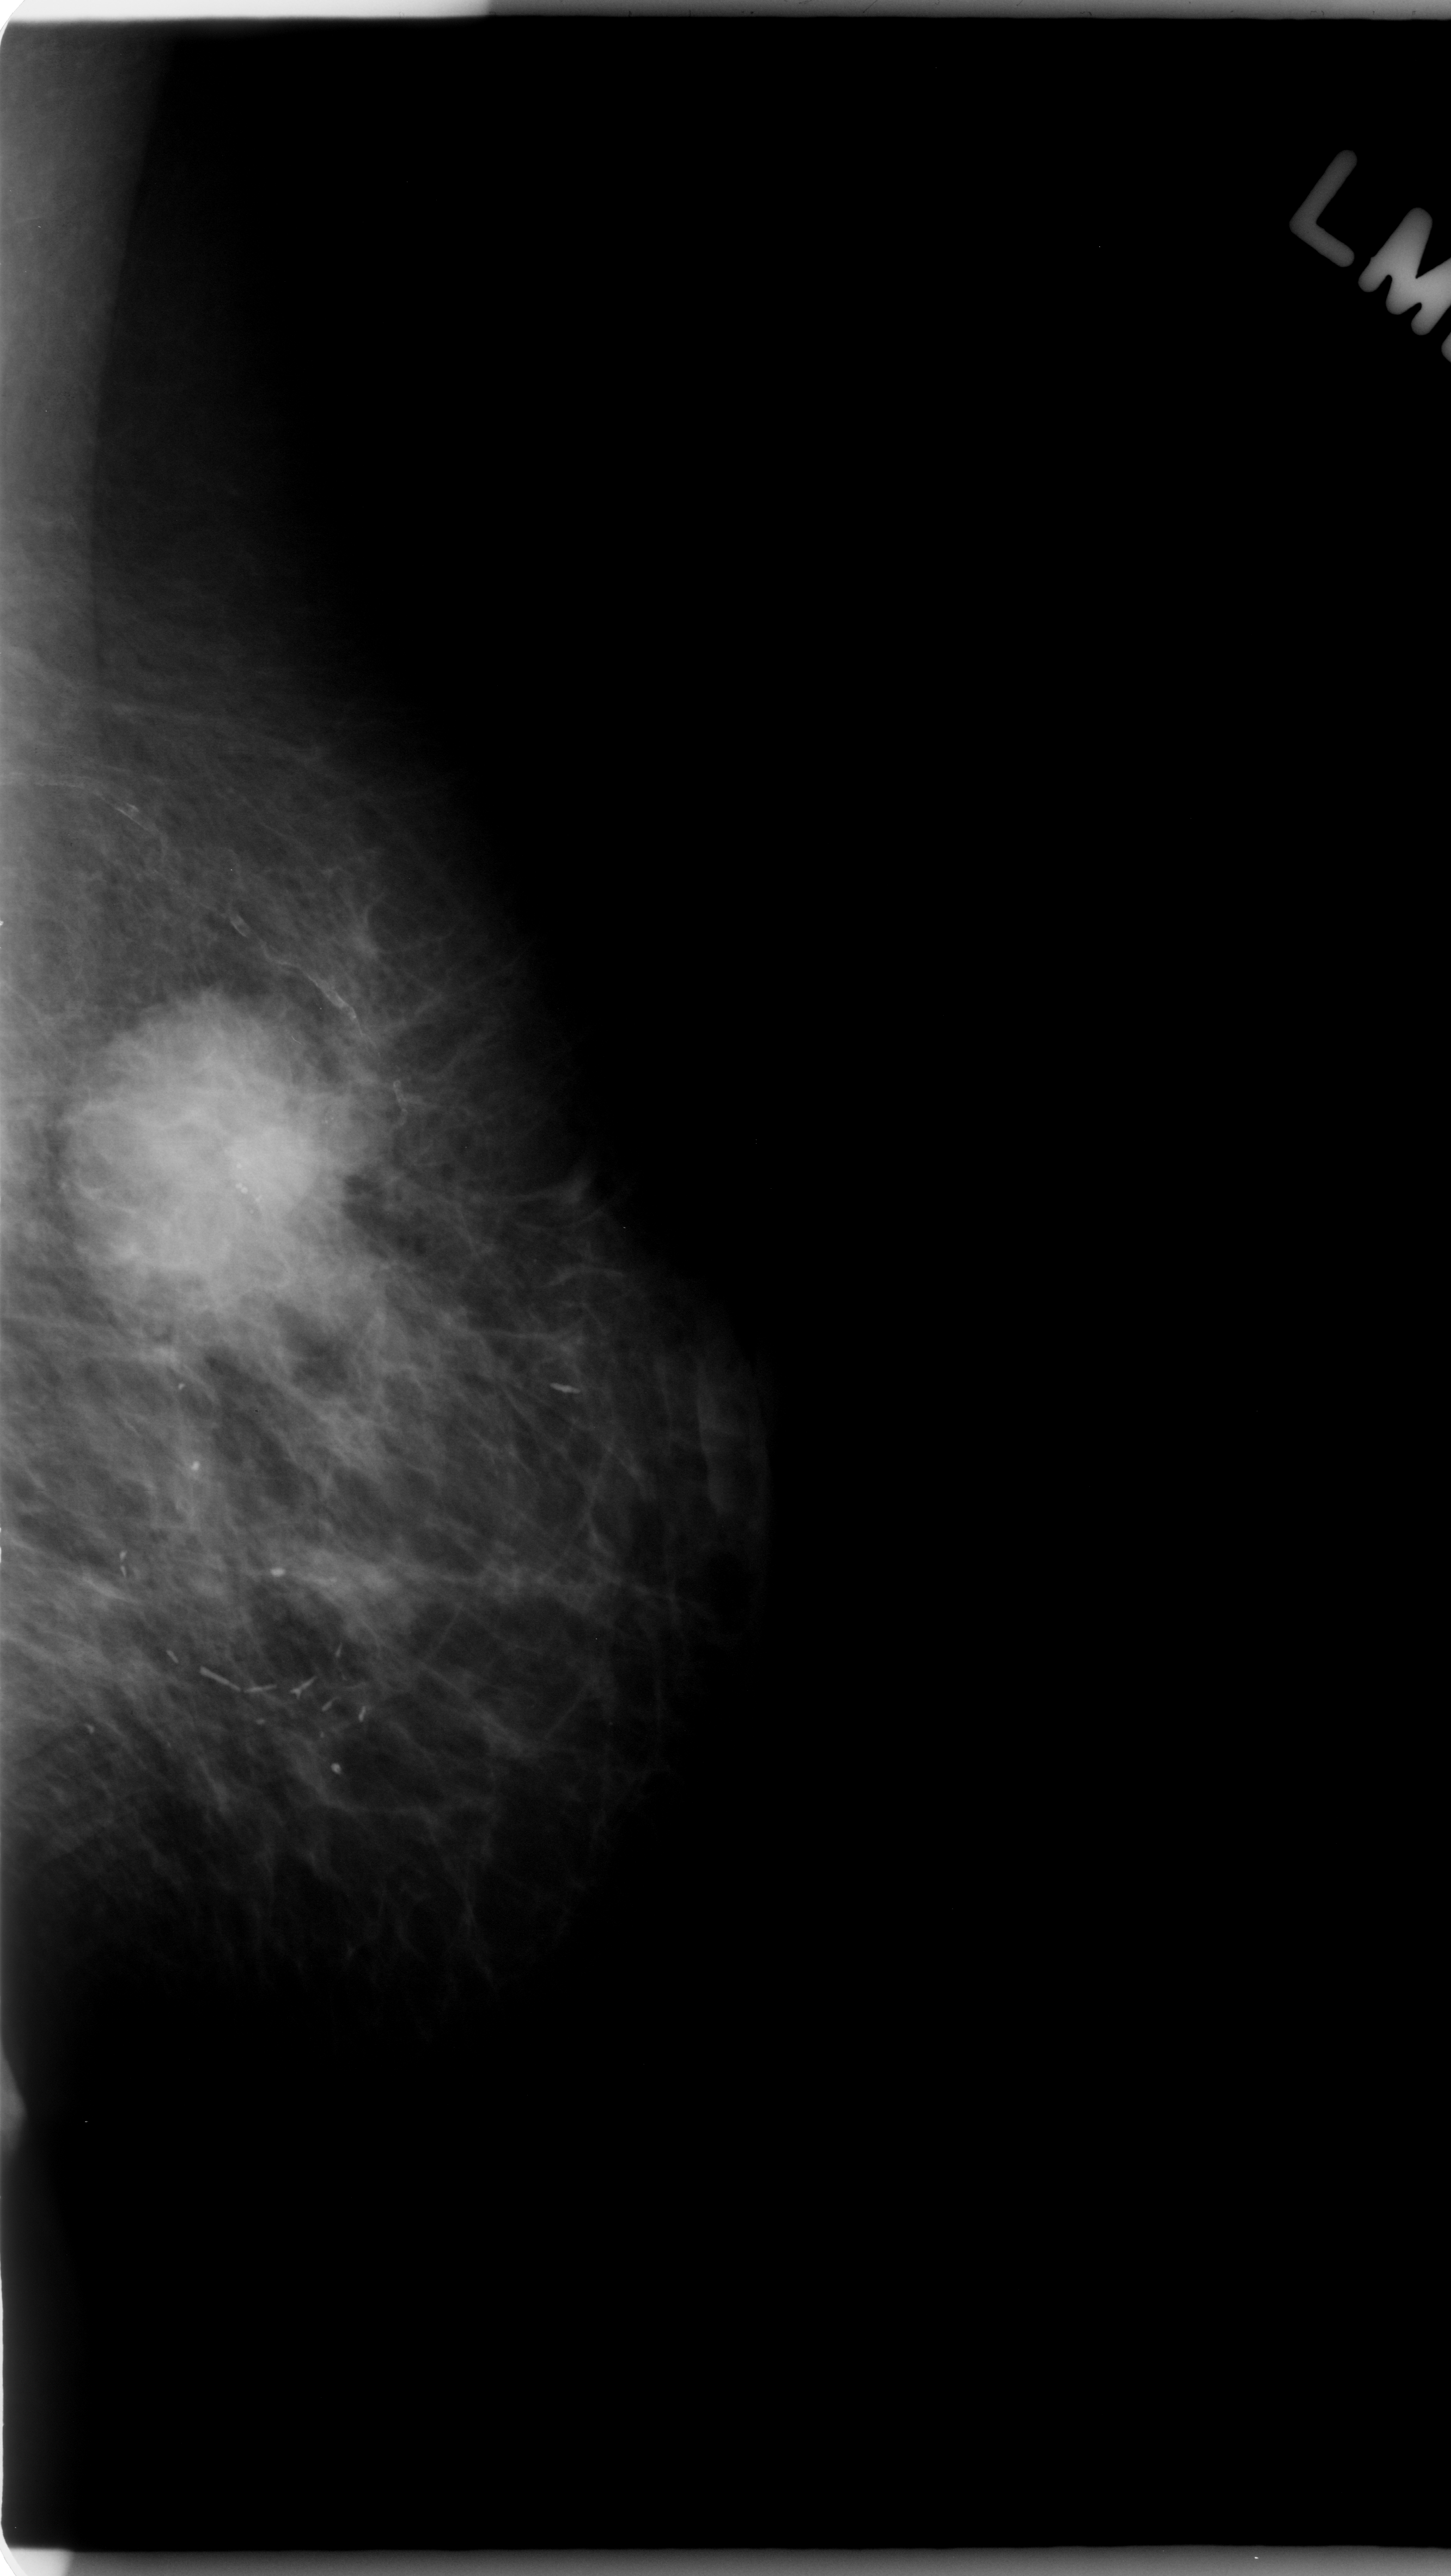
Mammogram (digitized film); left breast; mediolateral oblique (MLO) view; breast composition: almost entirely fatty (BI-RADS density category 1 of 4); 1451 × 2576 image matrix.
Expert-marked regions of interest on this film, with their recorded descriptors:
- mass, shape lobulated, margins microlobulated; BI-RADS assessment category 5; pathology result (as recorded, not read from the image): malignant: bounding box (x1, y1, x2, y2) in pixels: (83, 985, 346, 1300)